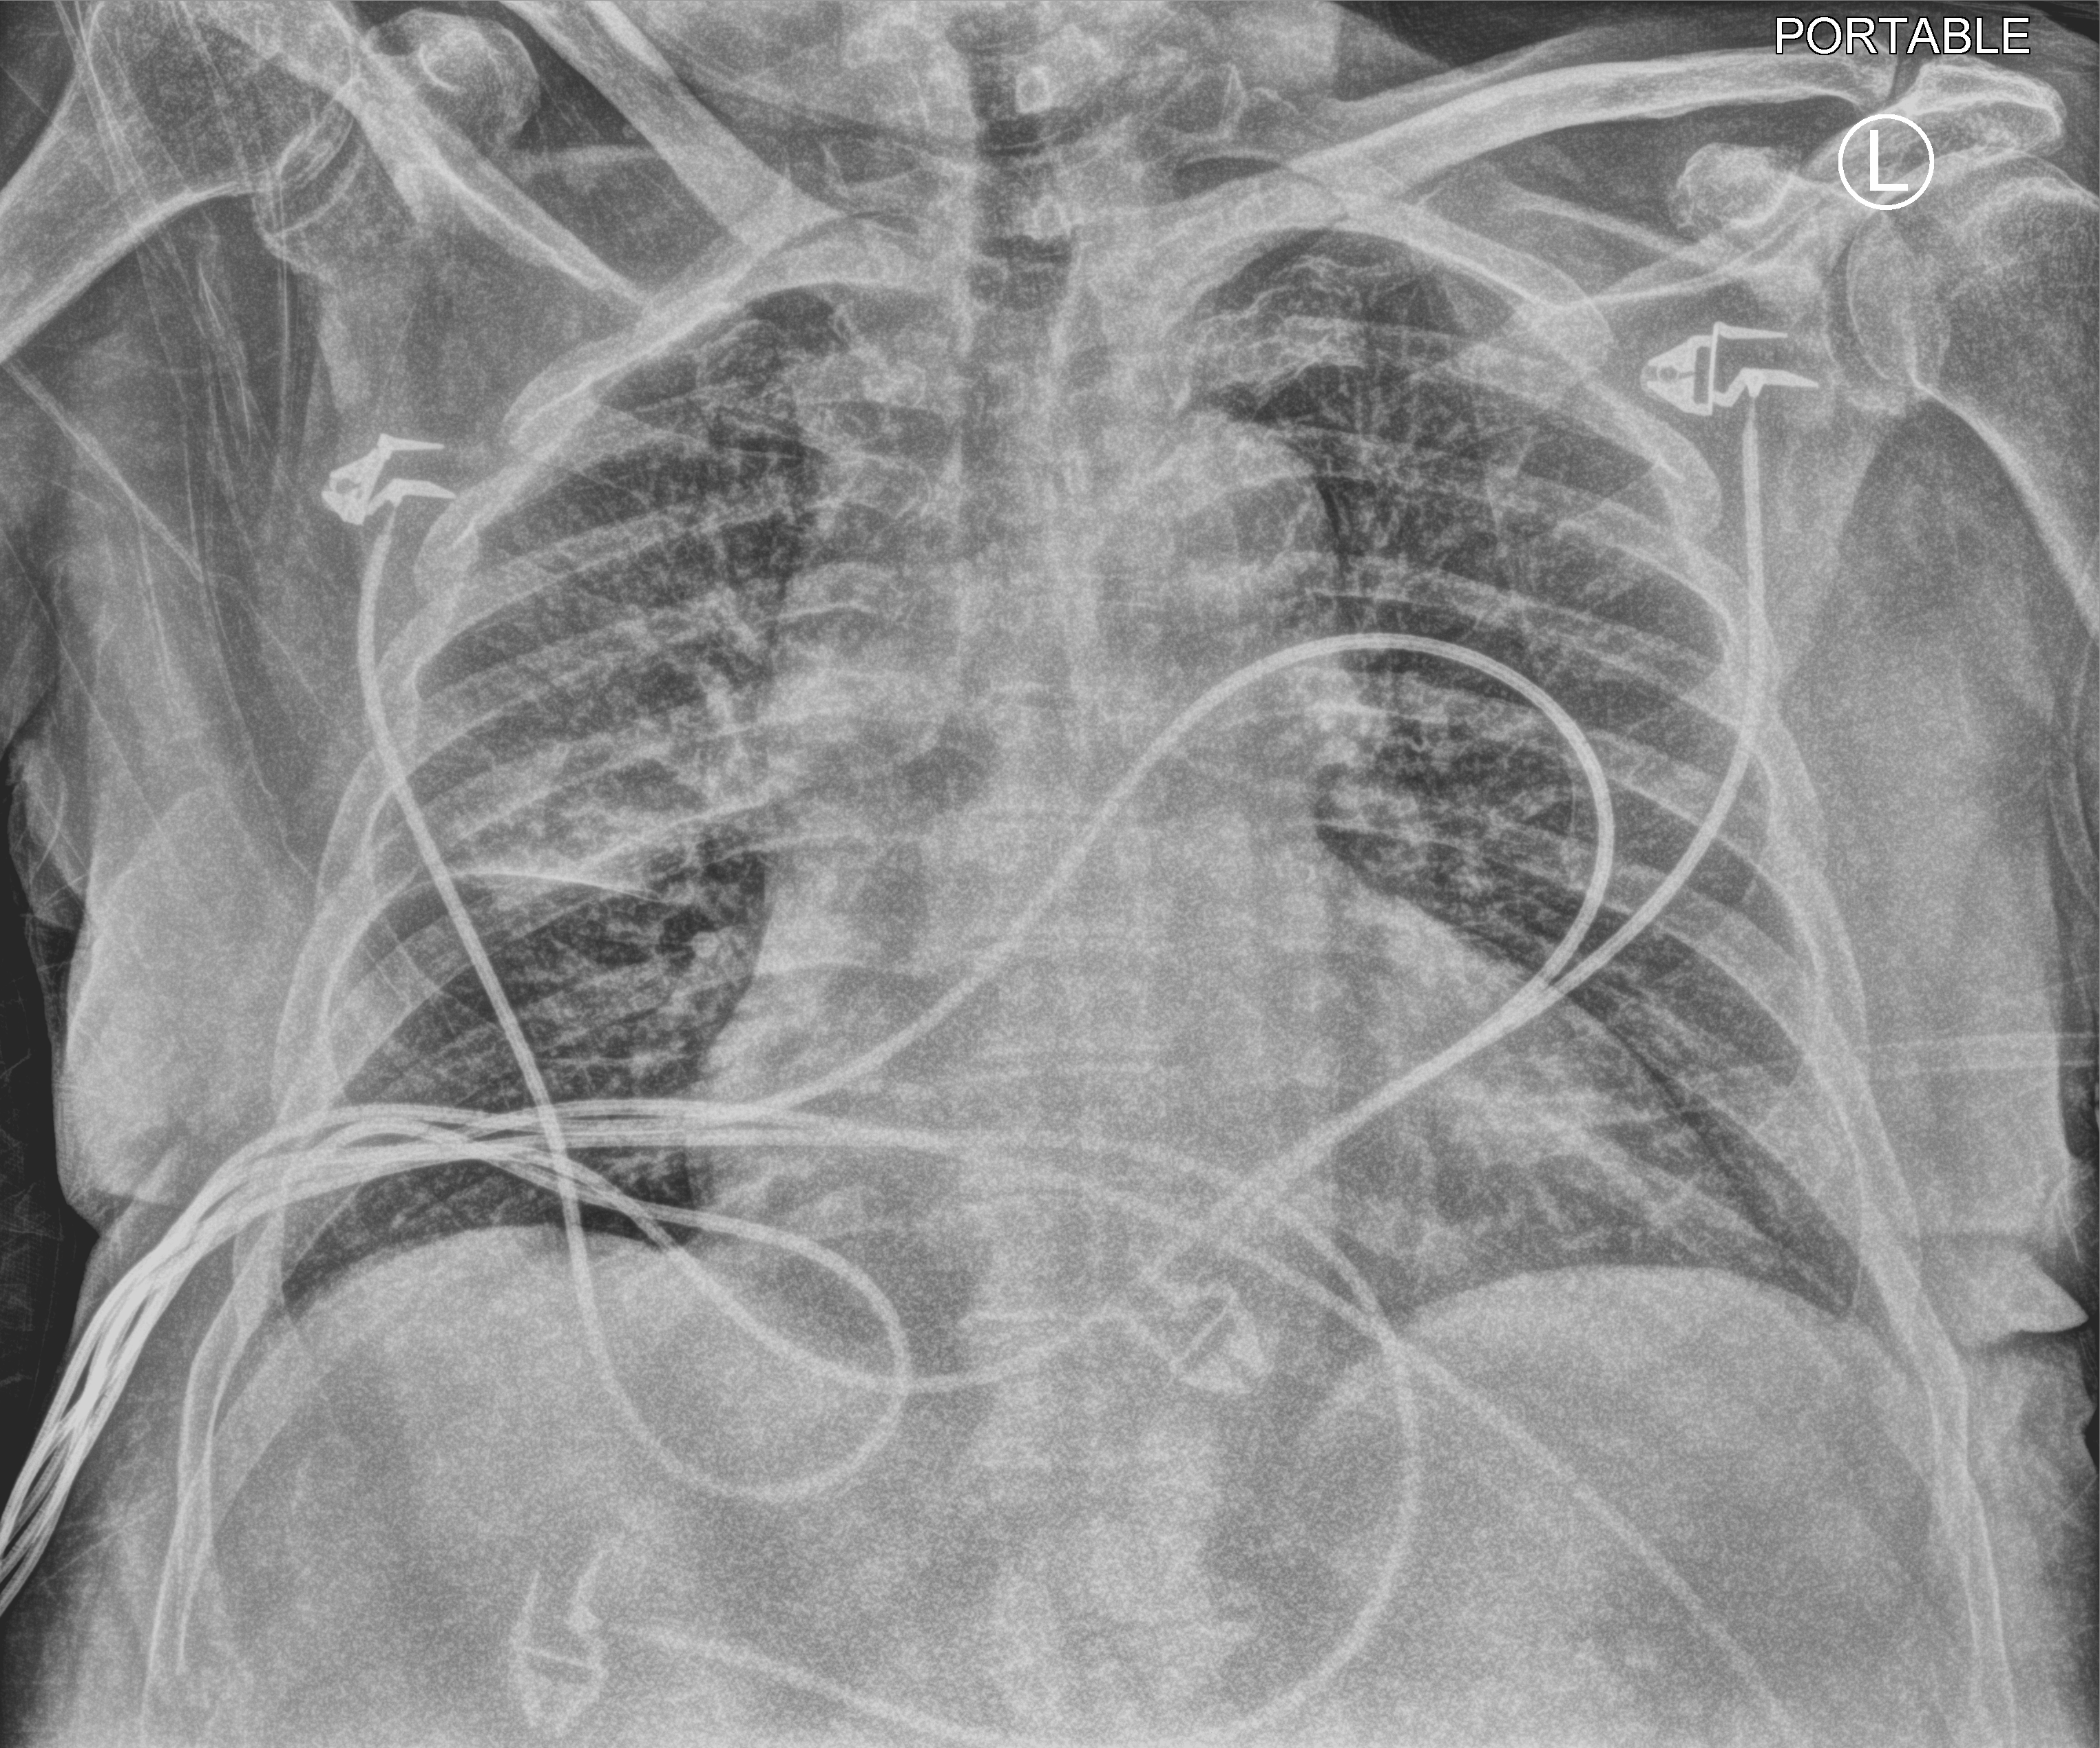
Chest X-ray (portable). Male patient hospitalised with COVID-19, age 75–90 years.
Admission-level facts for this patient (not findings on this image; timing relative to this image not recorded): diabetes (admission record): yes; smoking status (admission record): former.